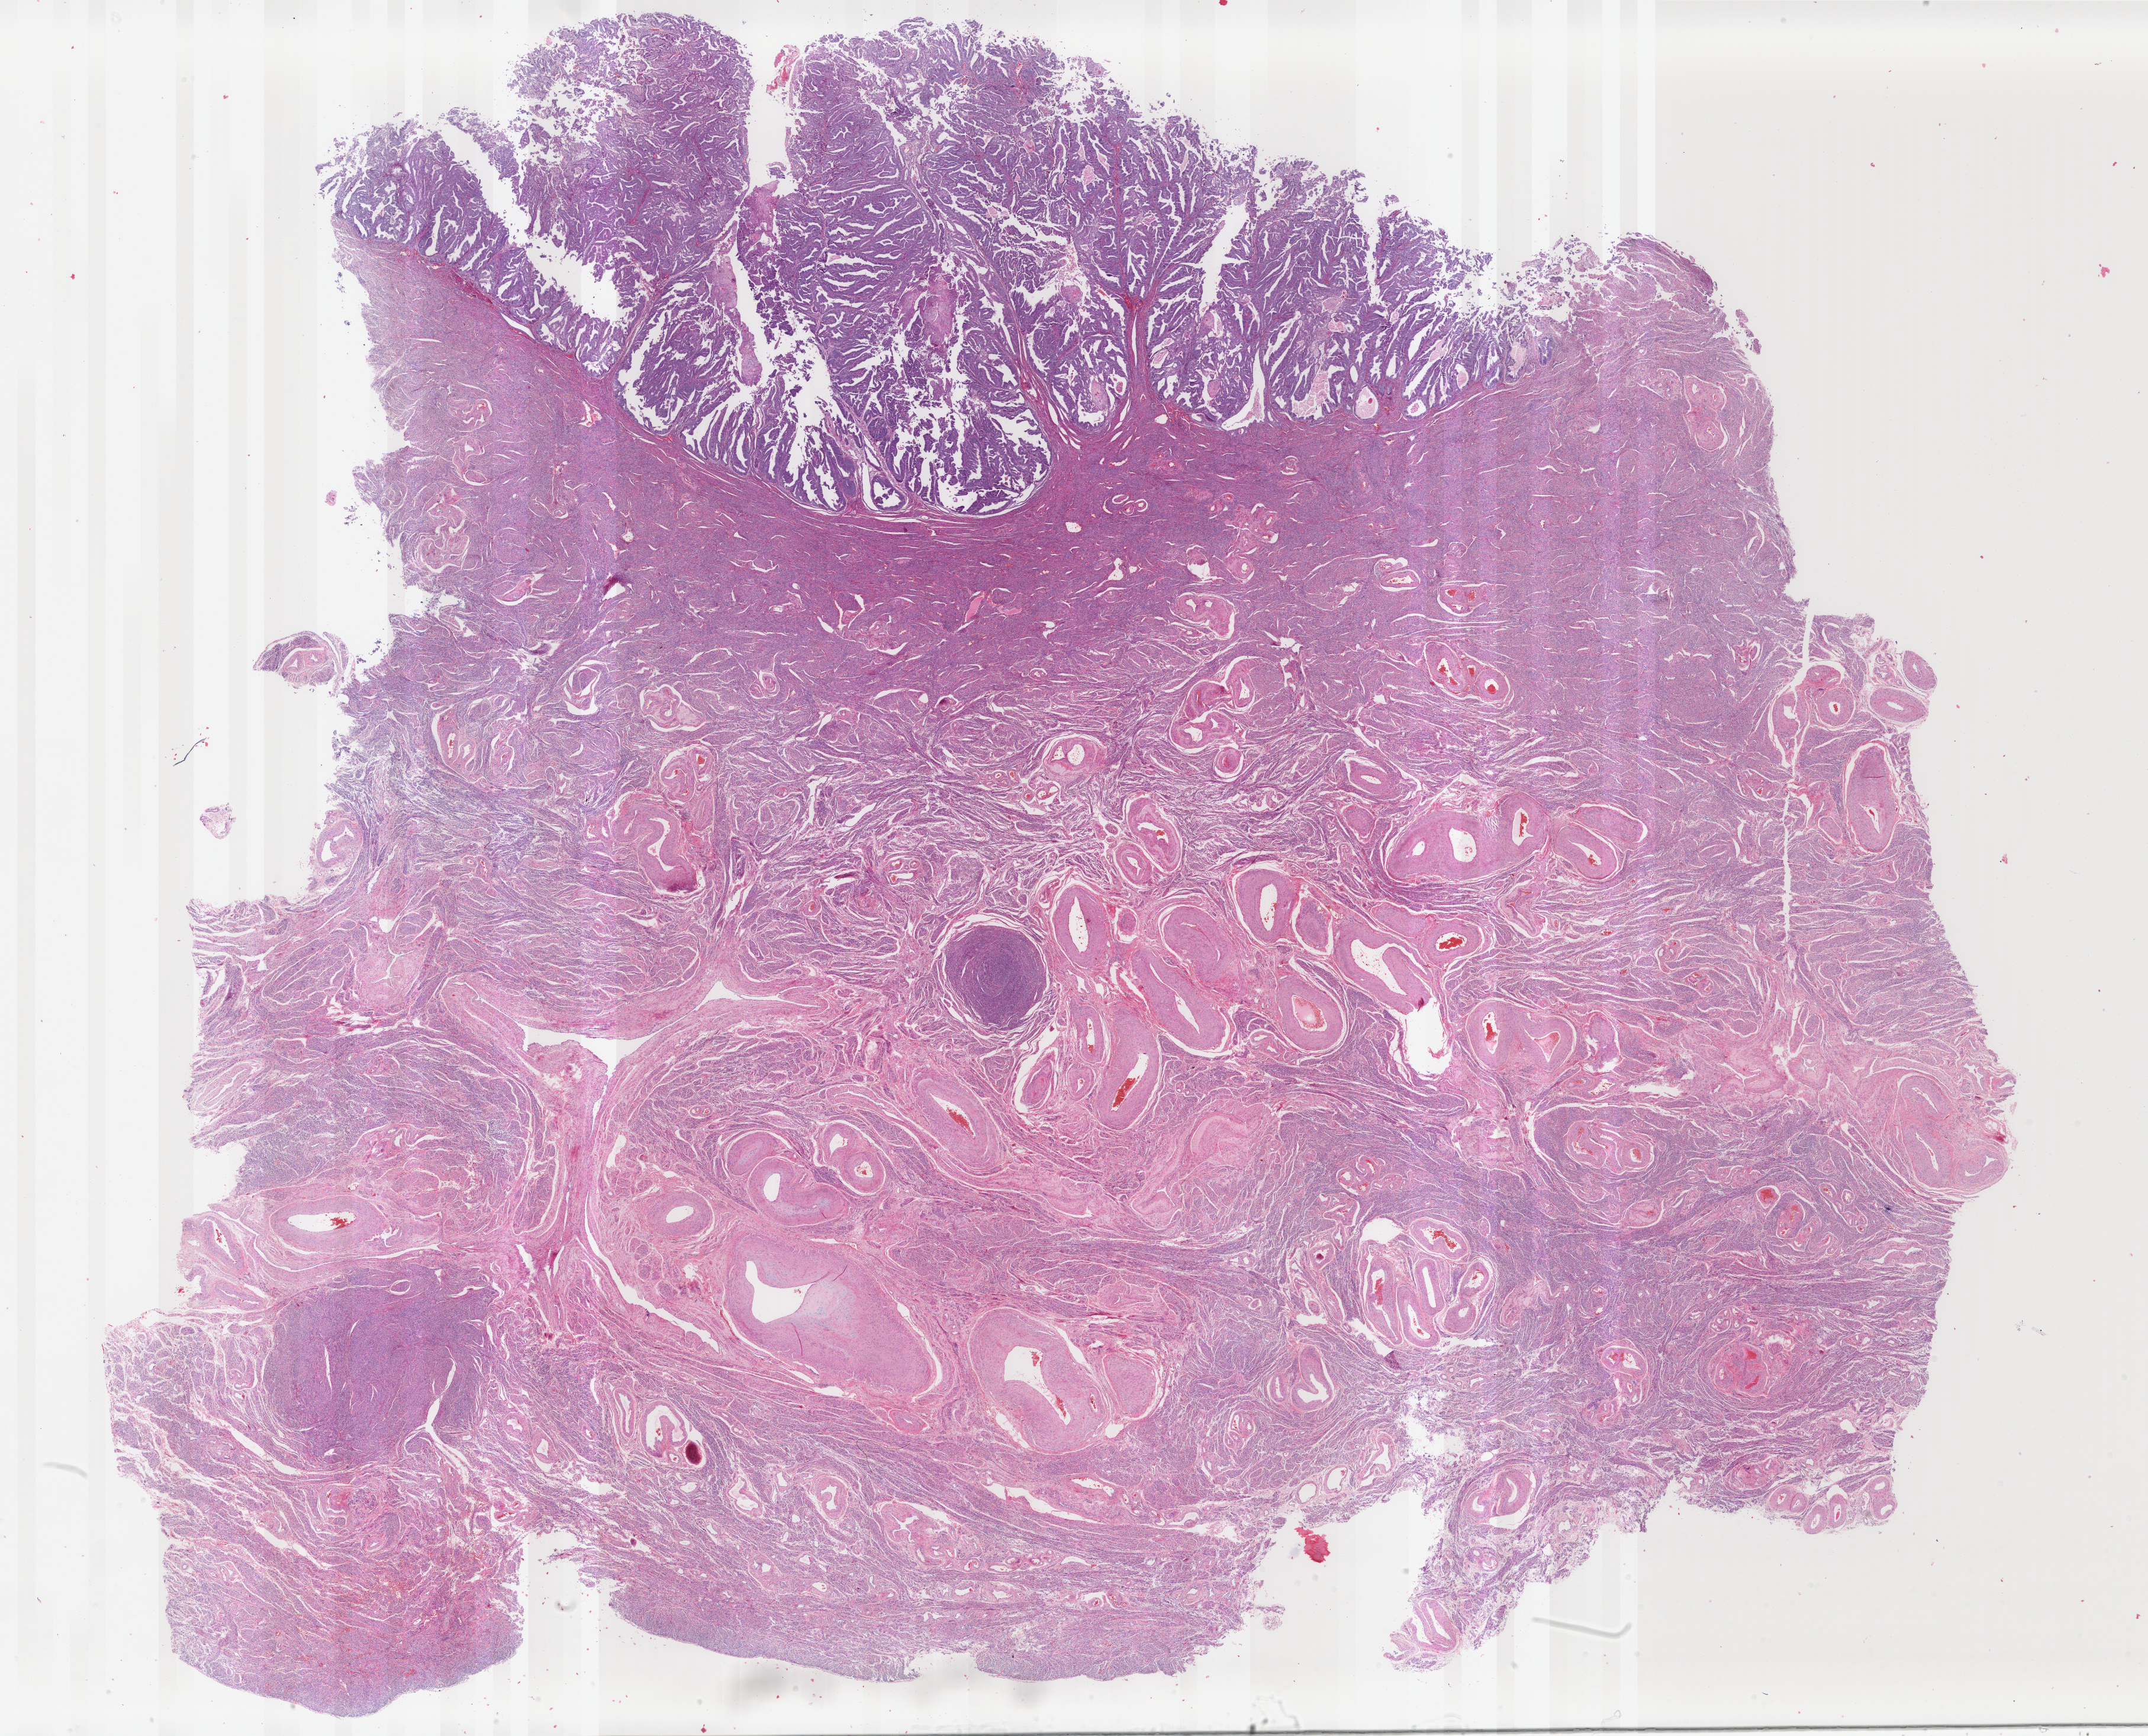
Digitized H&E tissue section (whole slide), a low-resolution overview of the entire scanned area, about 28.8 x 23.3 mm, formalin-fixed paraffin-embedded (FFPE) diagnostic section, sample: primary tumour, uterus. Patient: female, age at initial diagnosis 61 years.
Pathologic diagnosis: Endometrioid adenocarcinoma, NOS (endometrium).